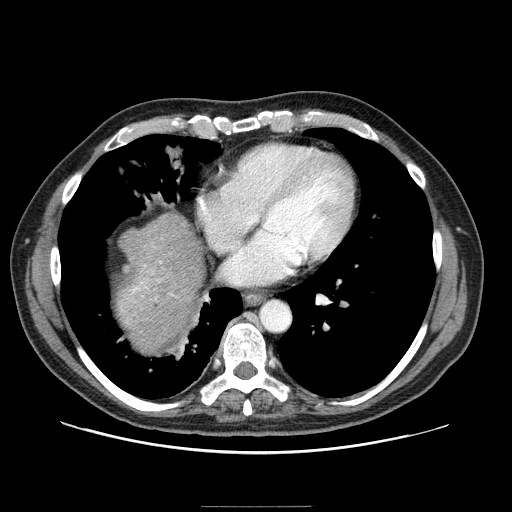
Contrast-enhanced abdominal CT (liver protocol), one axial slice; slice 86 of 99 in the series (ordered by position); 100 kVp; one of 2 acquisitions stored at this slice position; soft-tissue window (W 400 / L 40 HU); 512 × 512 image matrix, field of view 400 × 400 mm. From the clinical record (not read from this slice): diagnosis: hepatocellular carcinoma (patient treated with transarterial chemoembolisation; whether this scan precedes or follows treatment is not stated here); TNM stage (as recorded): Stage-II; Child-Pugh class: A; tumour differentiation: well differentiated; tumour nodularity: multinodular.
Structures marked on this image (semi-automatic segmentation, software-assisted and operator-edited):
- liver parenchyma outside the tumour (the mass and vessels are separate outlines, so this box may not span the whole liver): bounding box [x1, y1, x2, y2] px = [118, 214, 204, 350]
- liver vessels: [131, 262, 161, 293]